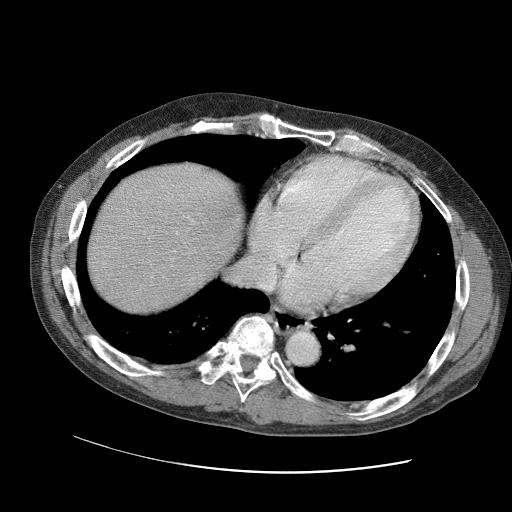
Contrast-enhanced abdominal CT (liver protocol), one axial slice; position 91 of 109 along the scan axis; reconstruction kernel STANDARD; 120 kVp; soft-tissue window (W 400 / L 40 HU); 512 × 512 image matrix, field of view 400 × 400 mm. Case-level facts recorded for this patient, not image findings: diagnosis: hepatocellular carcinoma (patient treated with transarterial chemoembolisation; whether this scan precedes or follows treatment is not stated here); TNM stage (as recorded): Stage-IIIC; Child-Pugh class: B; tumour nodularity: uninodular.
Structures marked on this image (semi-automatically segmented with operator editing):
- liver parenchyma outside the tumour (the mass and vessels are separate outlines, so this box may not span the whole liver): bounding box <85,162,242,312> (left, top, right, bottom; pixels)
- liver vessels: <144,193,195,281>